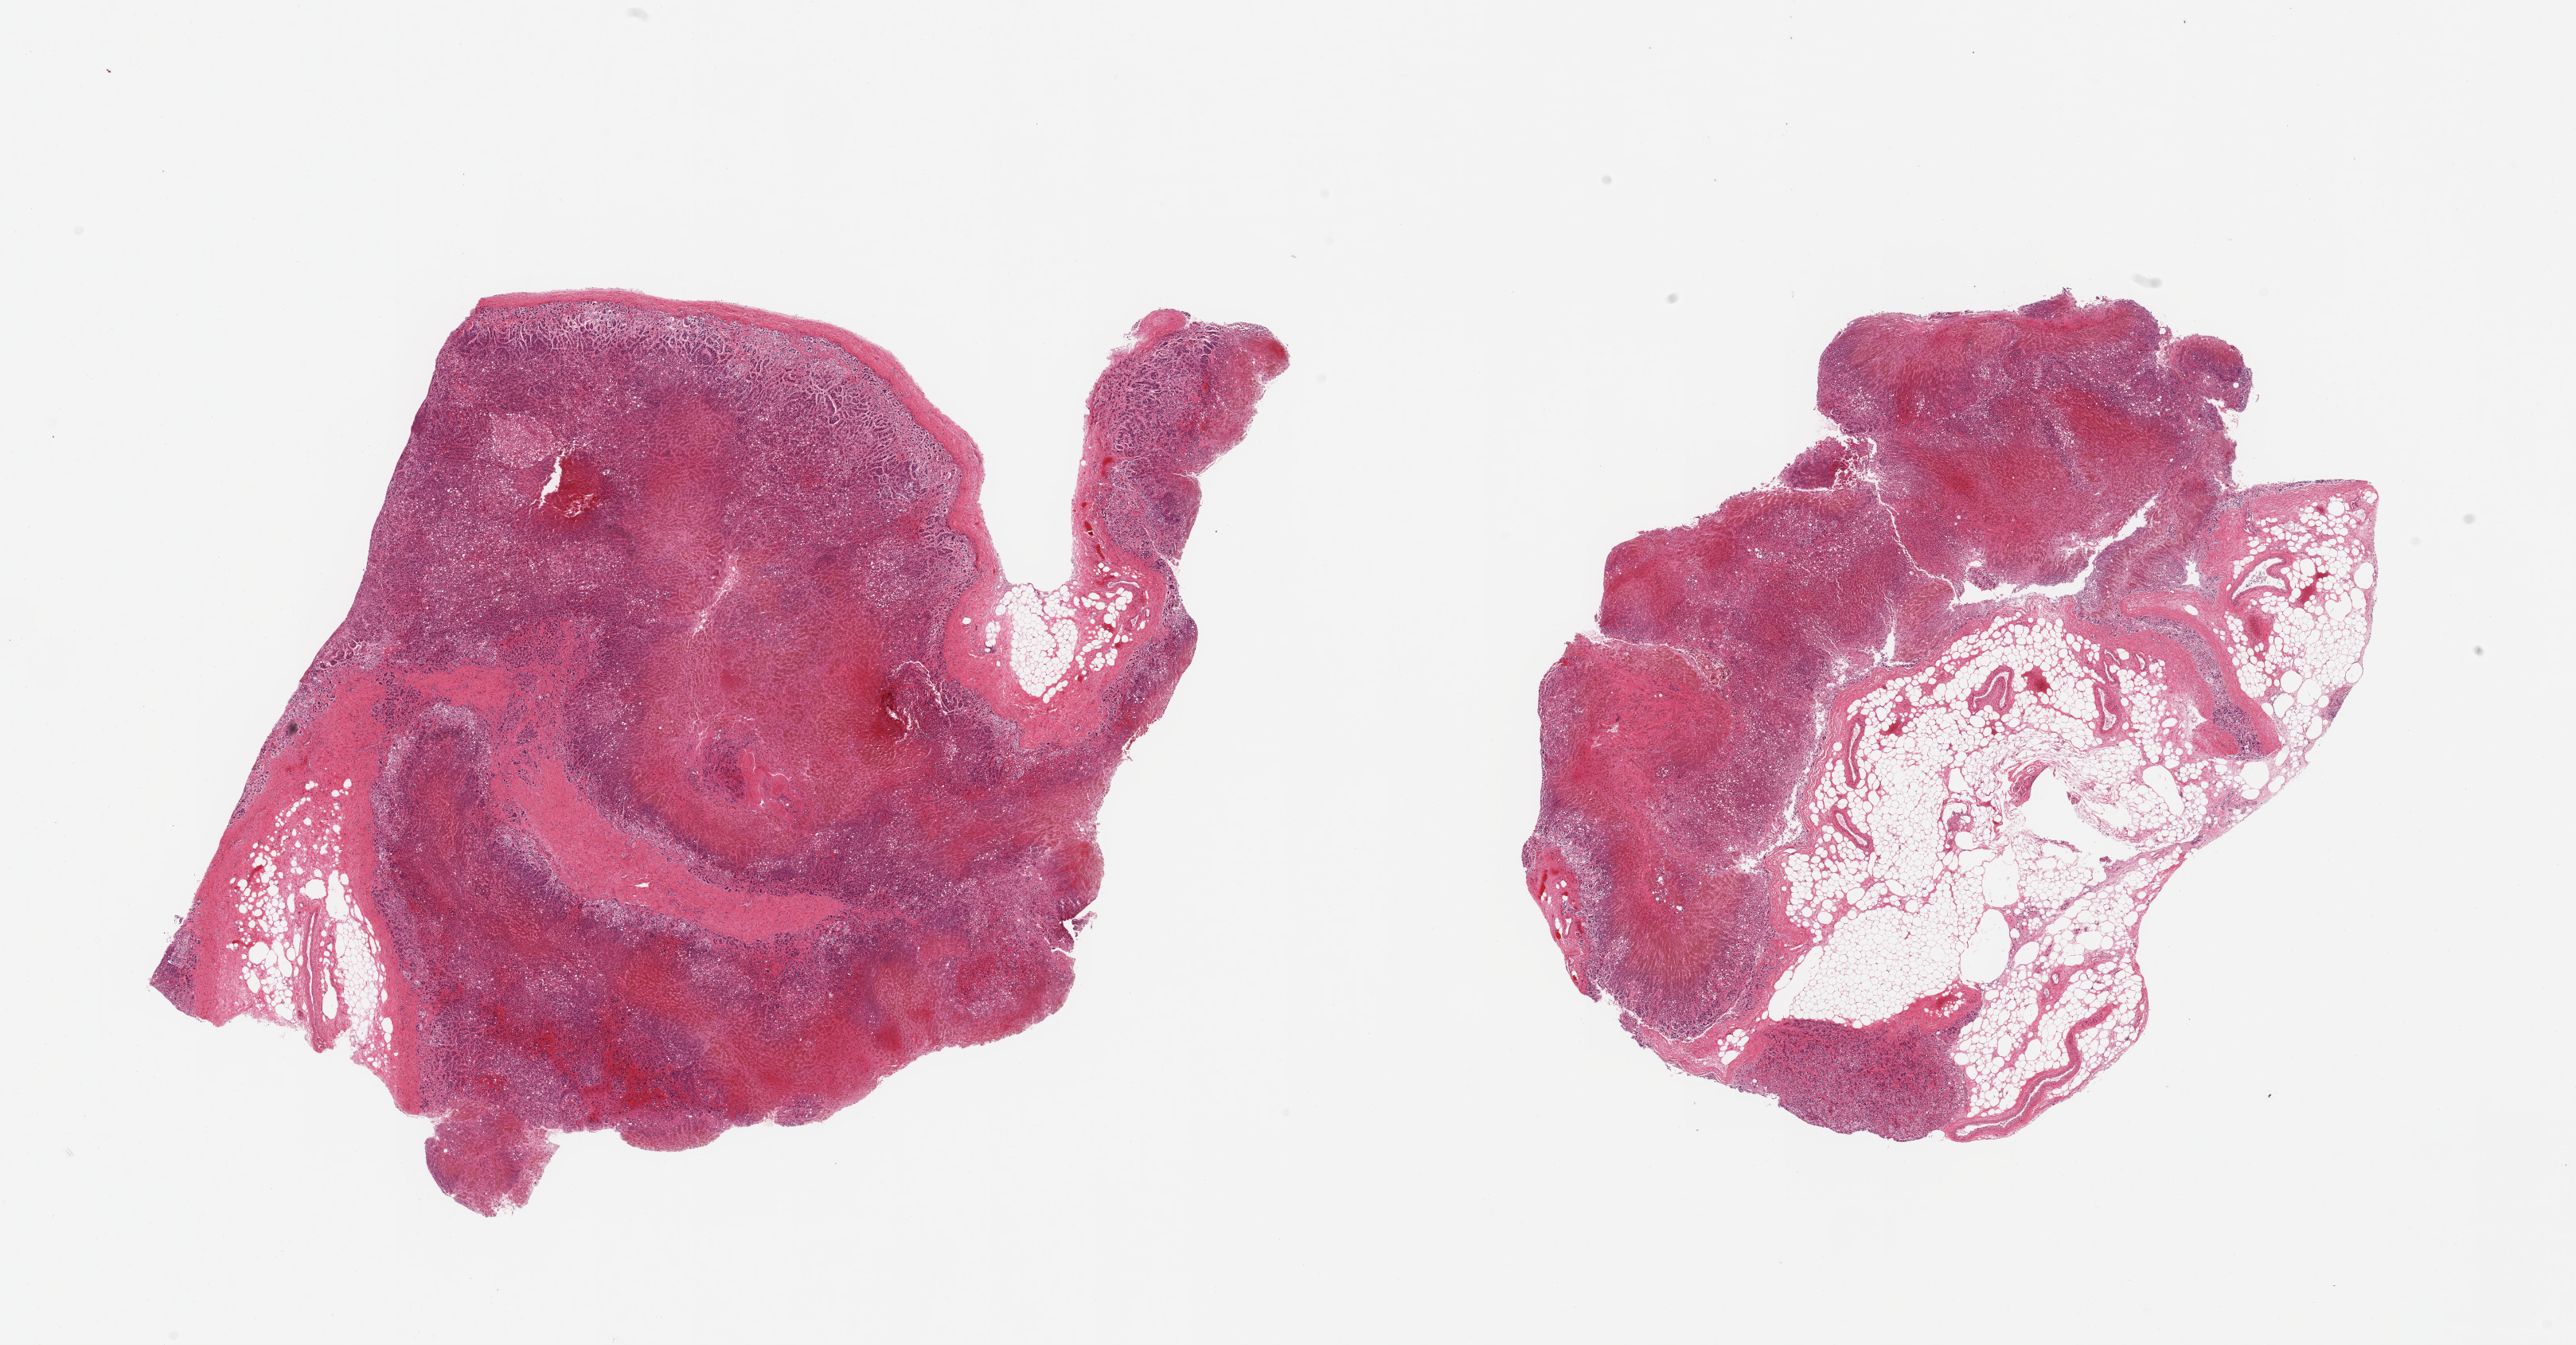
Whole-slide image, hematoxylin and eosin (H&E) stain — shown as a low-resolution overview of the whole scanned area (about 25.6 x 13.4 mm, from a 20x scan), PAXgene-fixed, paraffin-embedded tissue, sampled site (target tissue): adrenal gland, tissue donor sample. Female donor.
Reviewer comment on this tissue sample: 2 pieces; patchy areas [30%] appear infarcted; 1 piece has 50% fat.